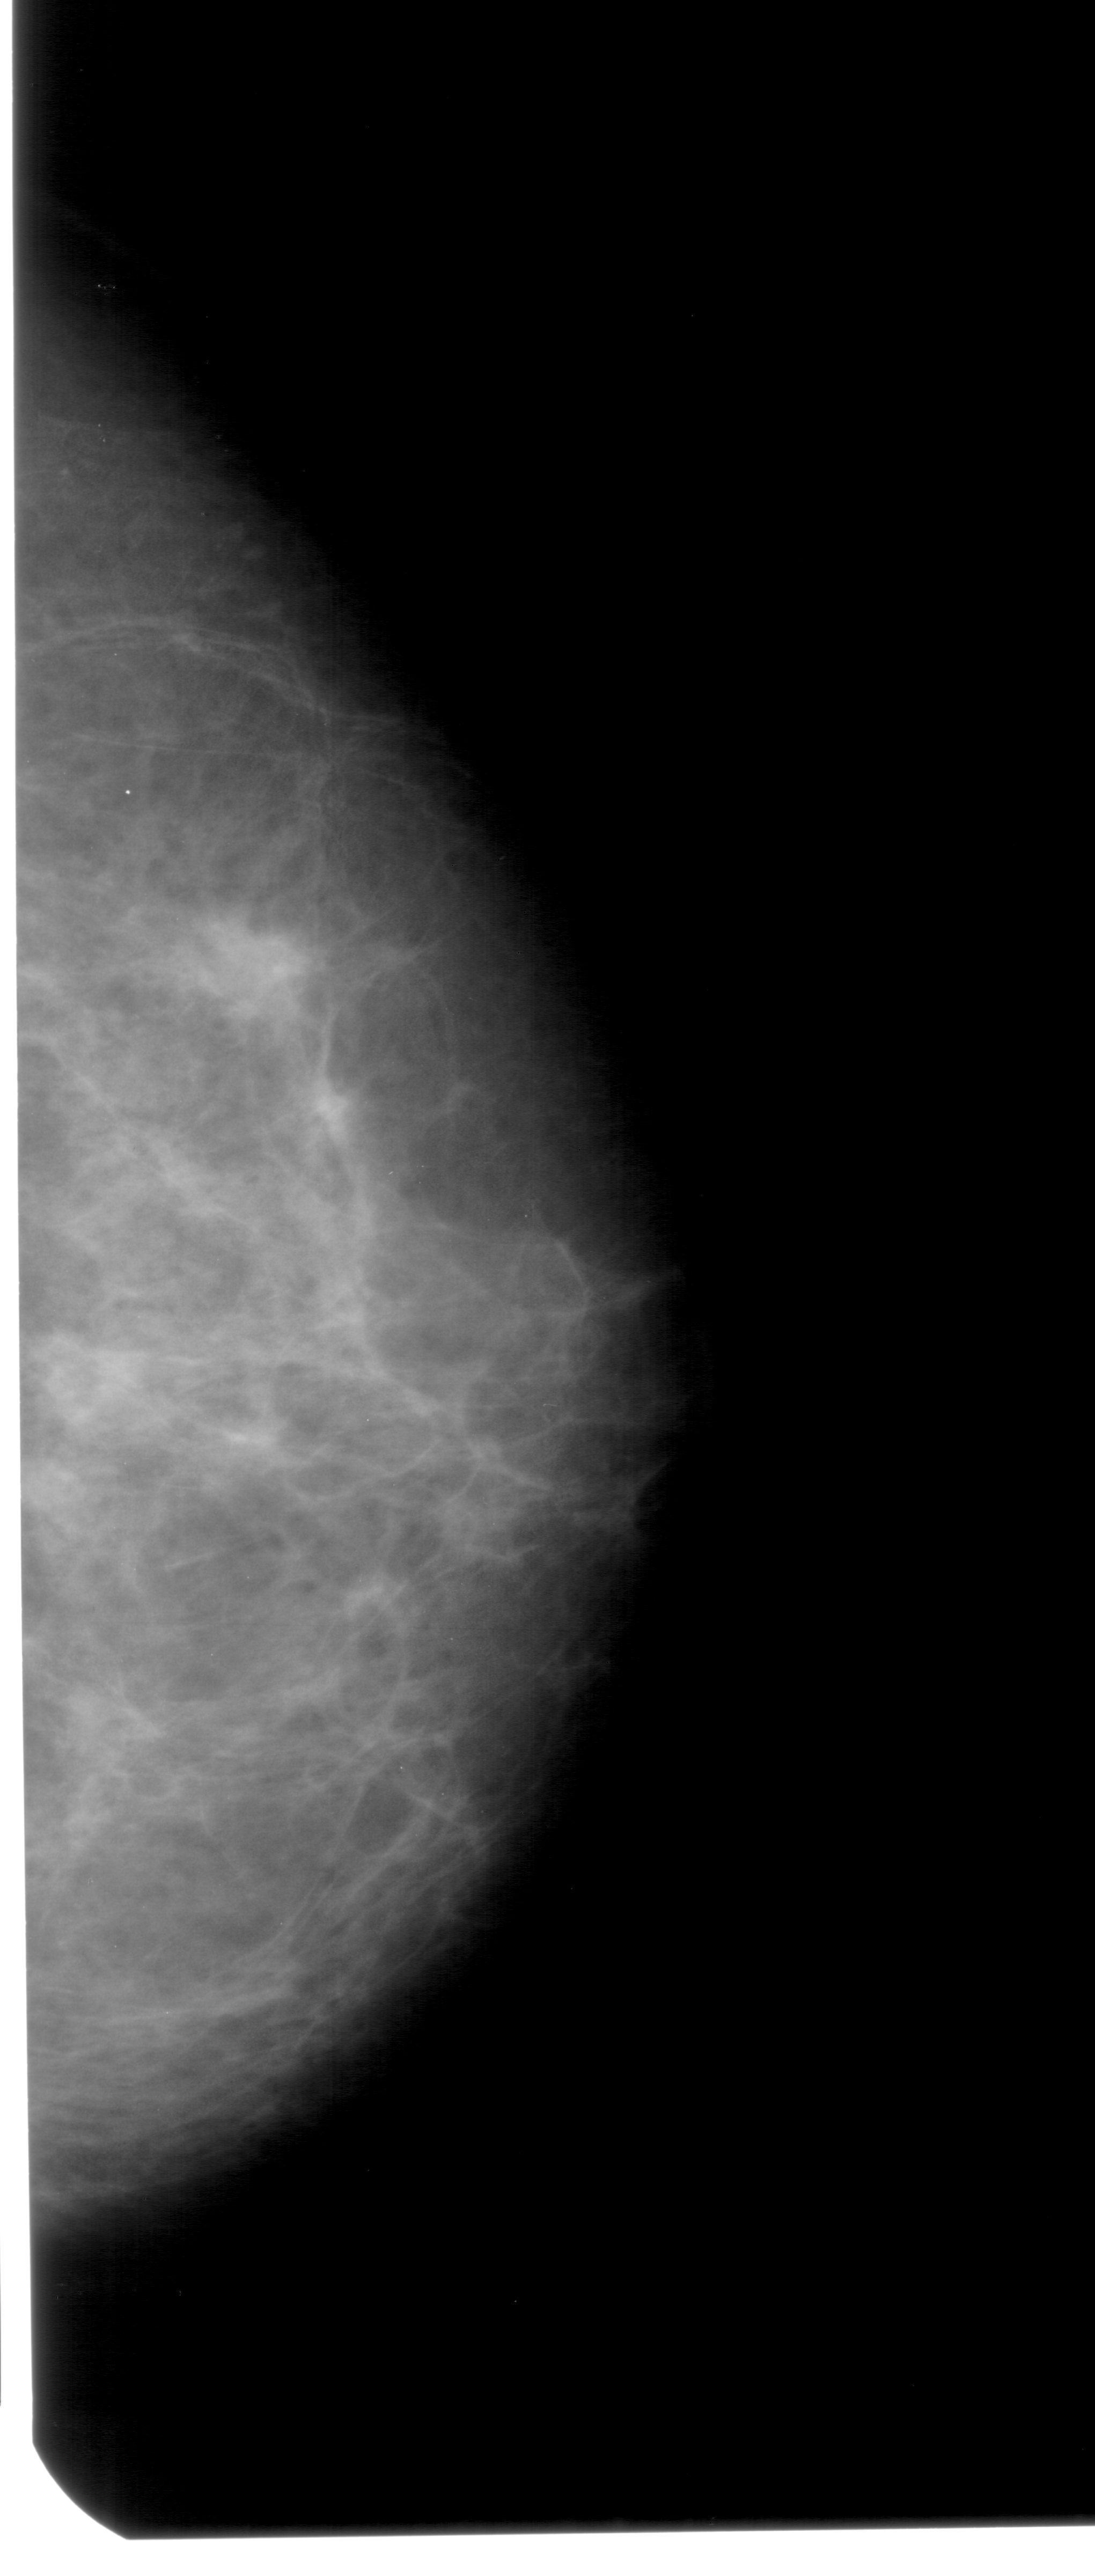
Digitized screen-film mammogram; right breast; CC view; breast composition: scattered fibroglandular densities (BI-RADS density category 2 of 4); 1095 × 2576 image matrix.
Expert-marked regions of interest on this image (one box per marked abnormality):
- mass, shape focal asymmetric density, margins ill defined; BI-RADS assessment category 4; pathology (as recorded): benign: box from (x=6, y=1325) to (x=176, y=1456) px